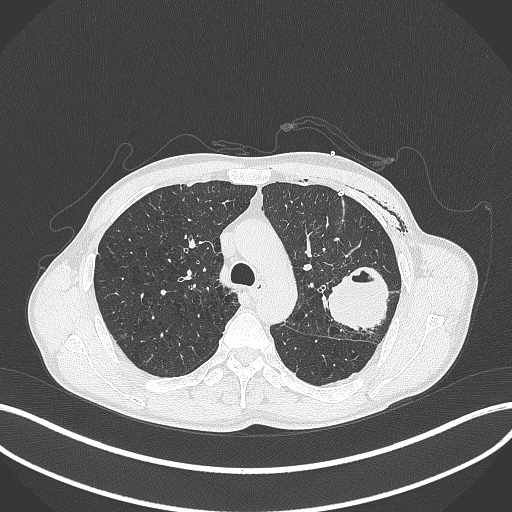
Chest CT, one axial slice. Position 284 of 457 along the scan axis. 120 kVp. Lung window (W 1500 / L -600 HU). 512 × 512 image matrix, field of view 400 × 400 mm. Patient: male, 58 years. From the clinical record (not read from this slice): clinical TNM (as recorded): T3 N0 M0.
Outlined on this slice (bounding box drawn by a radiologist):
- lung tumour (recorded histology: adenocarcinoma): bounding box [x1, y1, x2, y2] px = [325, 263, 390, 332]